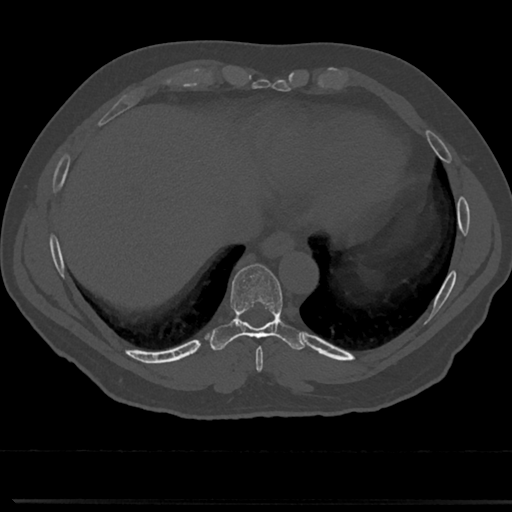
CT including the spine, one axial slice; slice 309 of 817 in the series (ordered by position); reconstruction kernel Br40s/3; bone window (W 1800 / L 400 HU); 0.5 mm slice thickness; 512 × 512 image matrix. Male patient, age 61 years. Case-level facts recorded for this patient, not image findings: primary cancer: prostate.
Outlined on this slice (semi-automatic segmentation, software-assisted and operator-edited):
- T8 vertebra: bounding box <232,271,288,354> (left, top, right, bottom; pixels)
- T9 vertebra: <232,267,282,328>